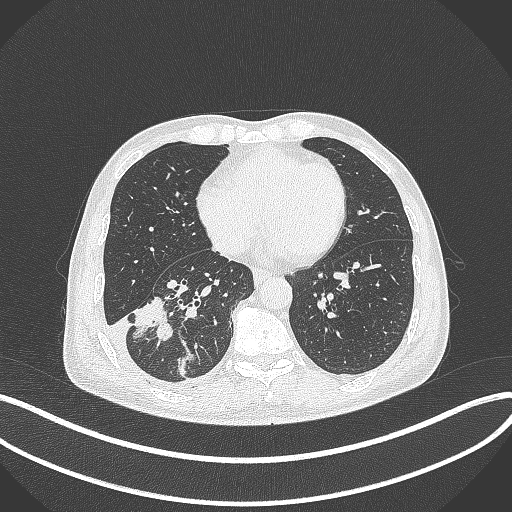
Chest CT, one axial slice. Reconstruction kernel B70f. 120 kVp. Lung window (W 1500 / L -600 HU). 1 mm slice thickness. 512 × 512 image matrix, field of view 400 × 400 mm. Patient: male, 64 years. Case-level facts recorded for this patient, not image findings: clinical TNM (as recorded): T3 N0 M0; histopathological grade: G2-3.
Annotated regions visible in this slice (bounding box drawn by a radiologist):
- lung tumour (recorded histology: adenocarcinoma): bounding box (x1, y1, x2, y2) in pixels: (131, 296, 174, 345)